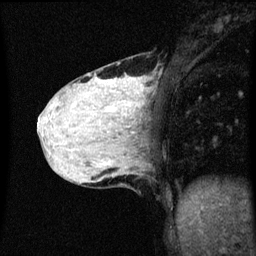
Breast MRI (dynamic contrast-enhanced), one sagittal slice; slice 20 of 60 in the series (ordered by position); dynamic contrast-enhanced series, image 2 of 3 at this slice position (ordered by acquisition); 1.5 T; TE 4.2 ms, TR 8.4 ms; 256 × 256 image matrix. Female patient, age 36 years.
Outlined on this slice (semi-automatic segmentation, software-assisted and operator-edited):
- analysis volume of interest (the breast-tissue region the enhancement analysis was run in; not a lesion): bounding box <48,64,151,151> (left, top, right, bottom; pixels)
- tumour enhancement mask (voxels above the 70 % enhancement threshold inside the analysis volume of interest): <110,78,145,127>